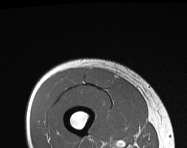
MRI of an extremity soft-tissue mass, one axial slice; MR volume resampled by the dataset authors to the PET/CT grid (not the native acquisition matrix); 3.27 mm slice thickness; 187 × 148 image matrix, field of view 183 × 145 mm. Male patient. From the clinical record (not read from this slice): histological type: pleiomorphic leiomyosarcoma; grade: intermediate; site of the primary tumour: right thigh.
Structures marked on this image (expert contour drawn on MRI and transferred to this co-registered scan by the dataset authors):
- gross tumour volume including surrounding oedema: bounding box [x1, y1, x2, y2] px = [86, 68, 112, 89]